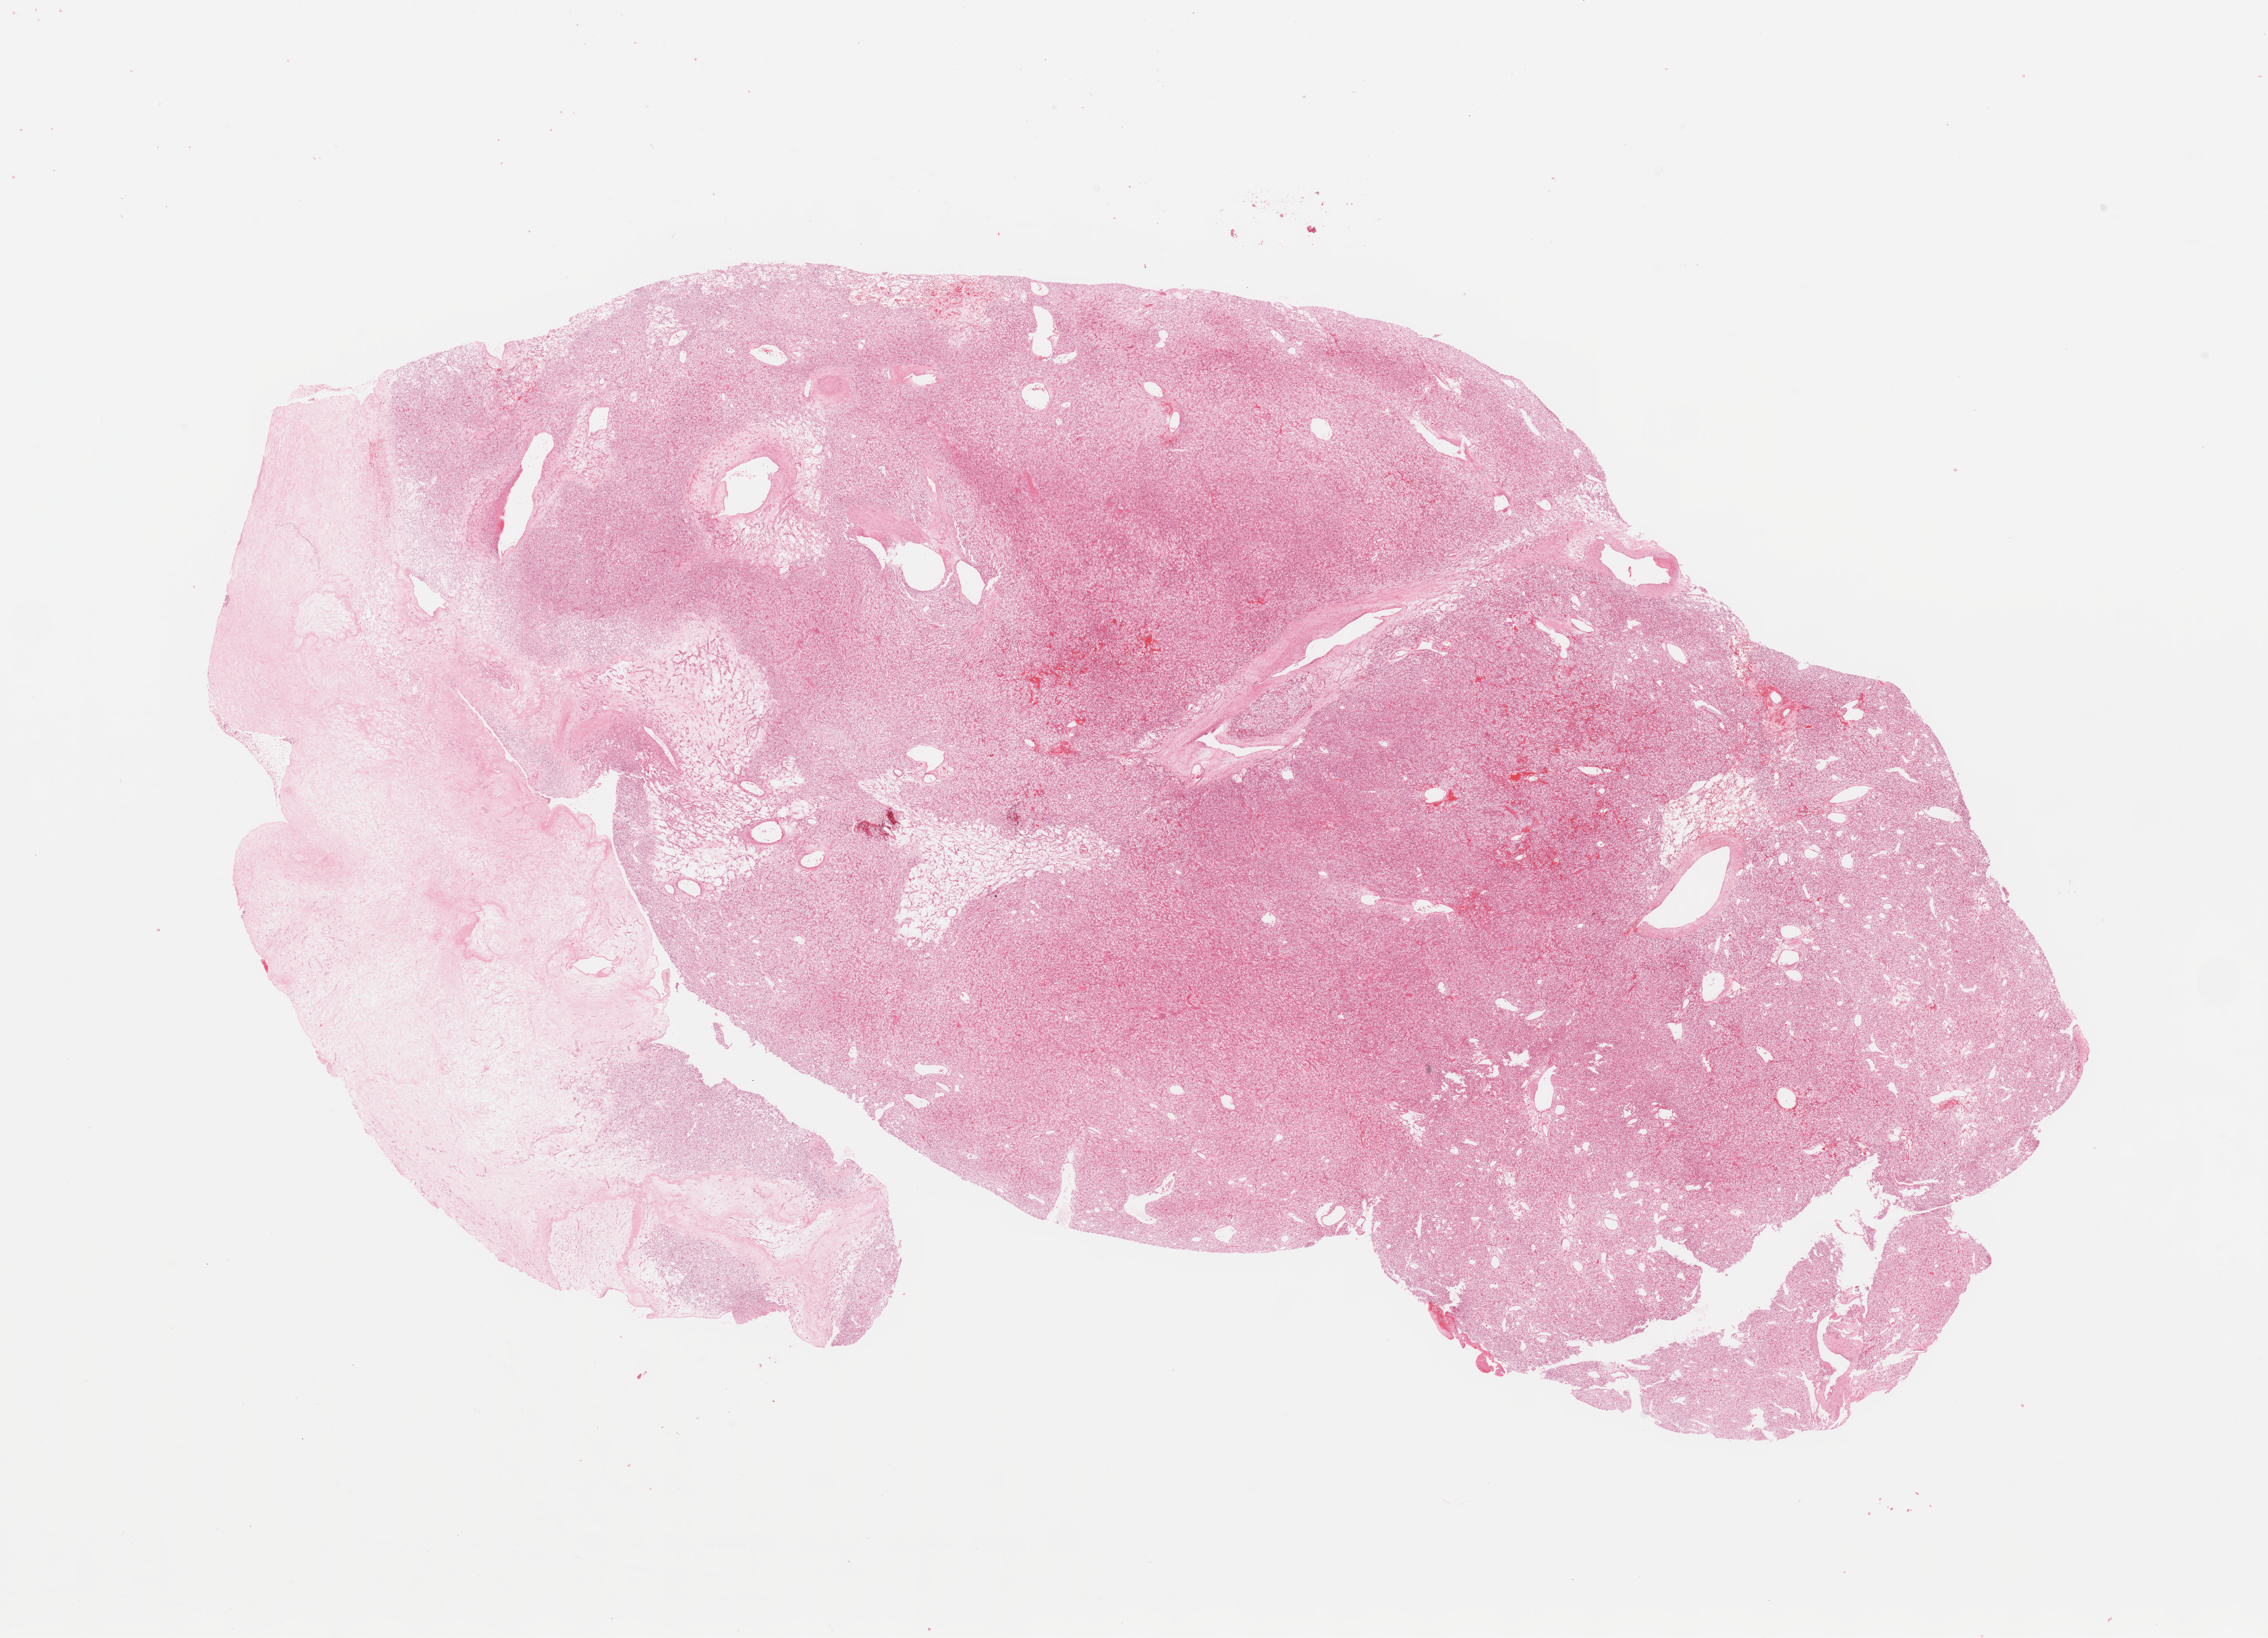
Whole-slide histology image, H&E-stained, shown as a low-resolution overview of the whole scanned area (about 26.6 x 19.2 mm, from a 20x scan), tumour tissue sample, kidney. Female, 41 y/o. Histologic grade: G2 (moderately differentiated).
Histologic diagnosis: Renal cell carcinoma, NOS. Primary tumour site (as recorded): lower pole.